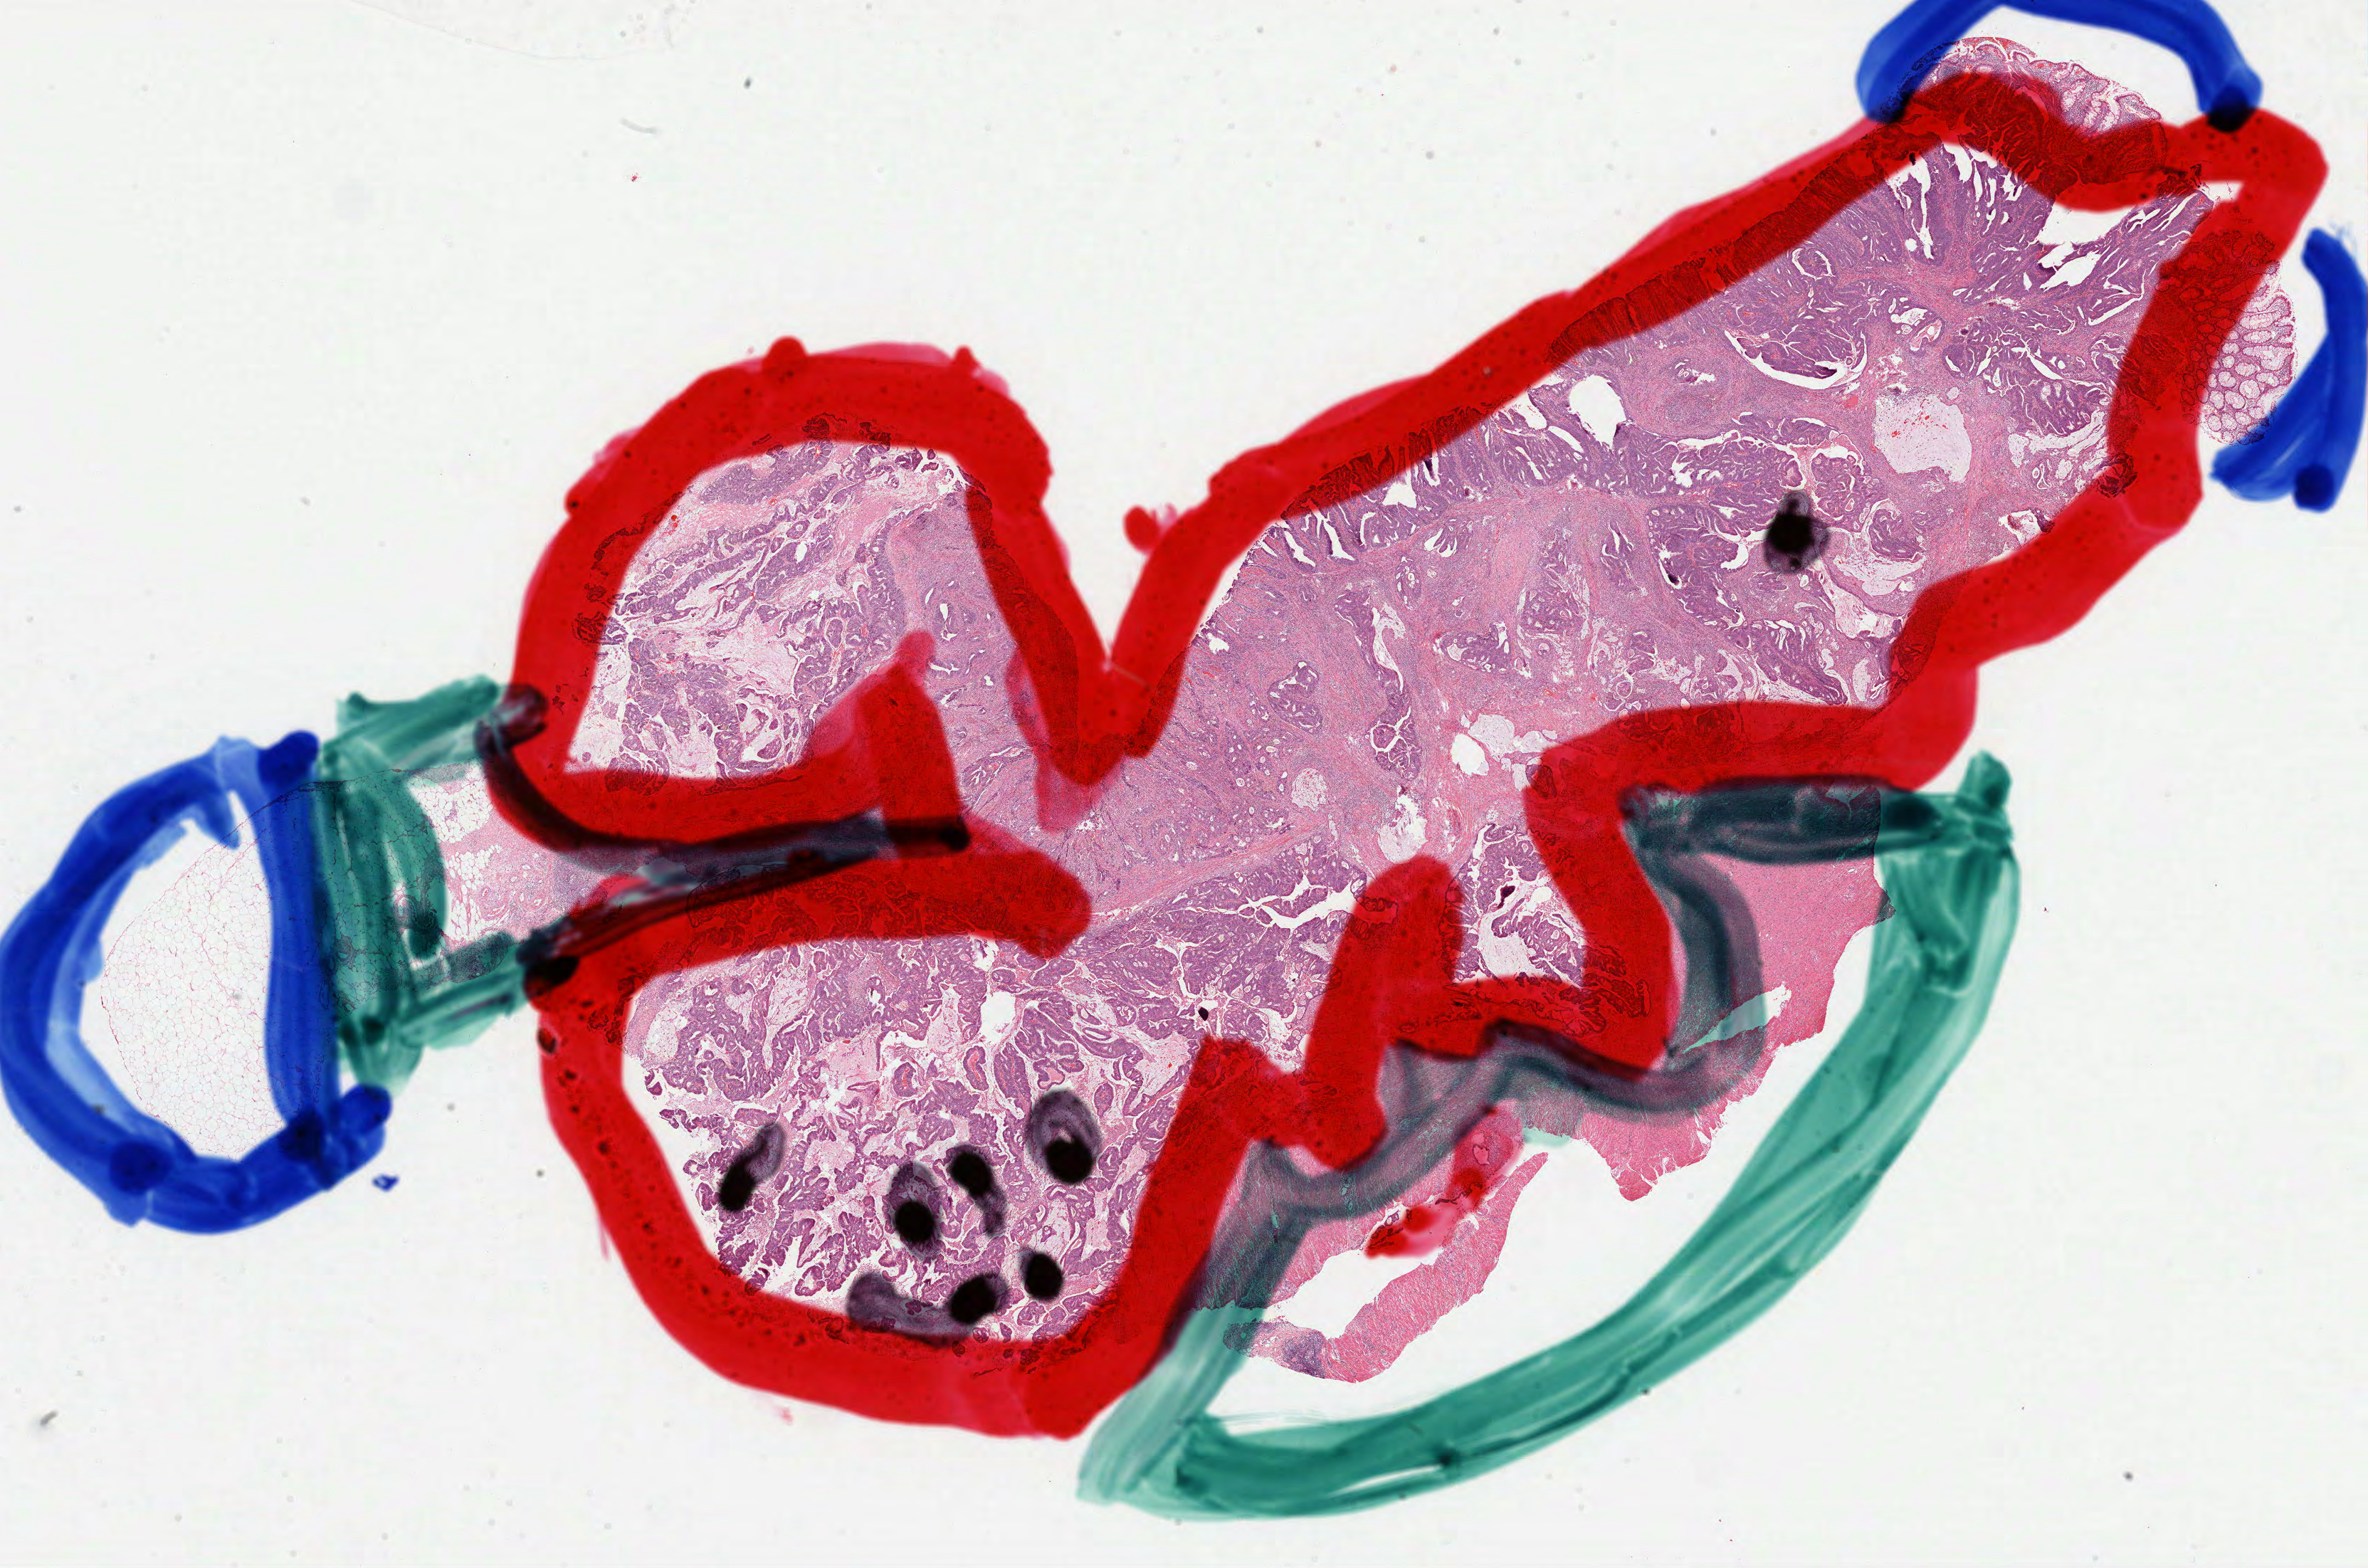
Whole-slide histology image, H&E, a low-resolution overview of the entire scanned area, about 26.8 x 17.8 mm (from a 40x scan), formalin-fixed paraffin-embedded (FFPE) diagnostic section, rectum, primary tumour sample. Patient: female, age at initial diagnosis 60 years.
Histologic diagnosis: Adenocarcinoma, NOS.